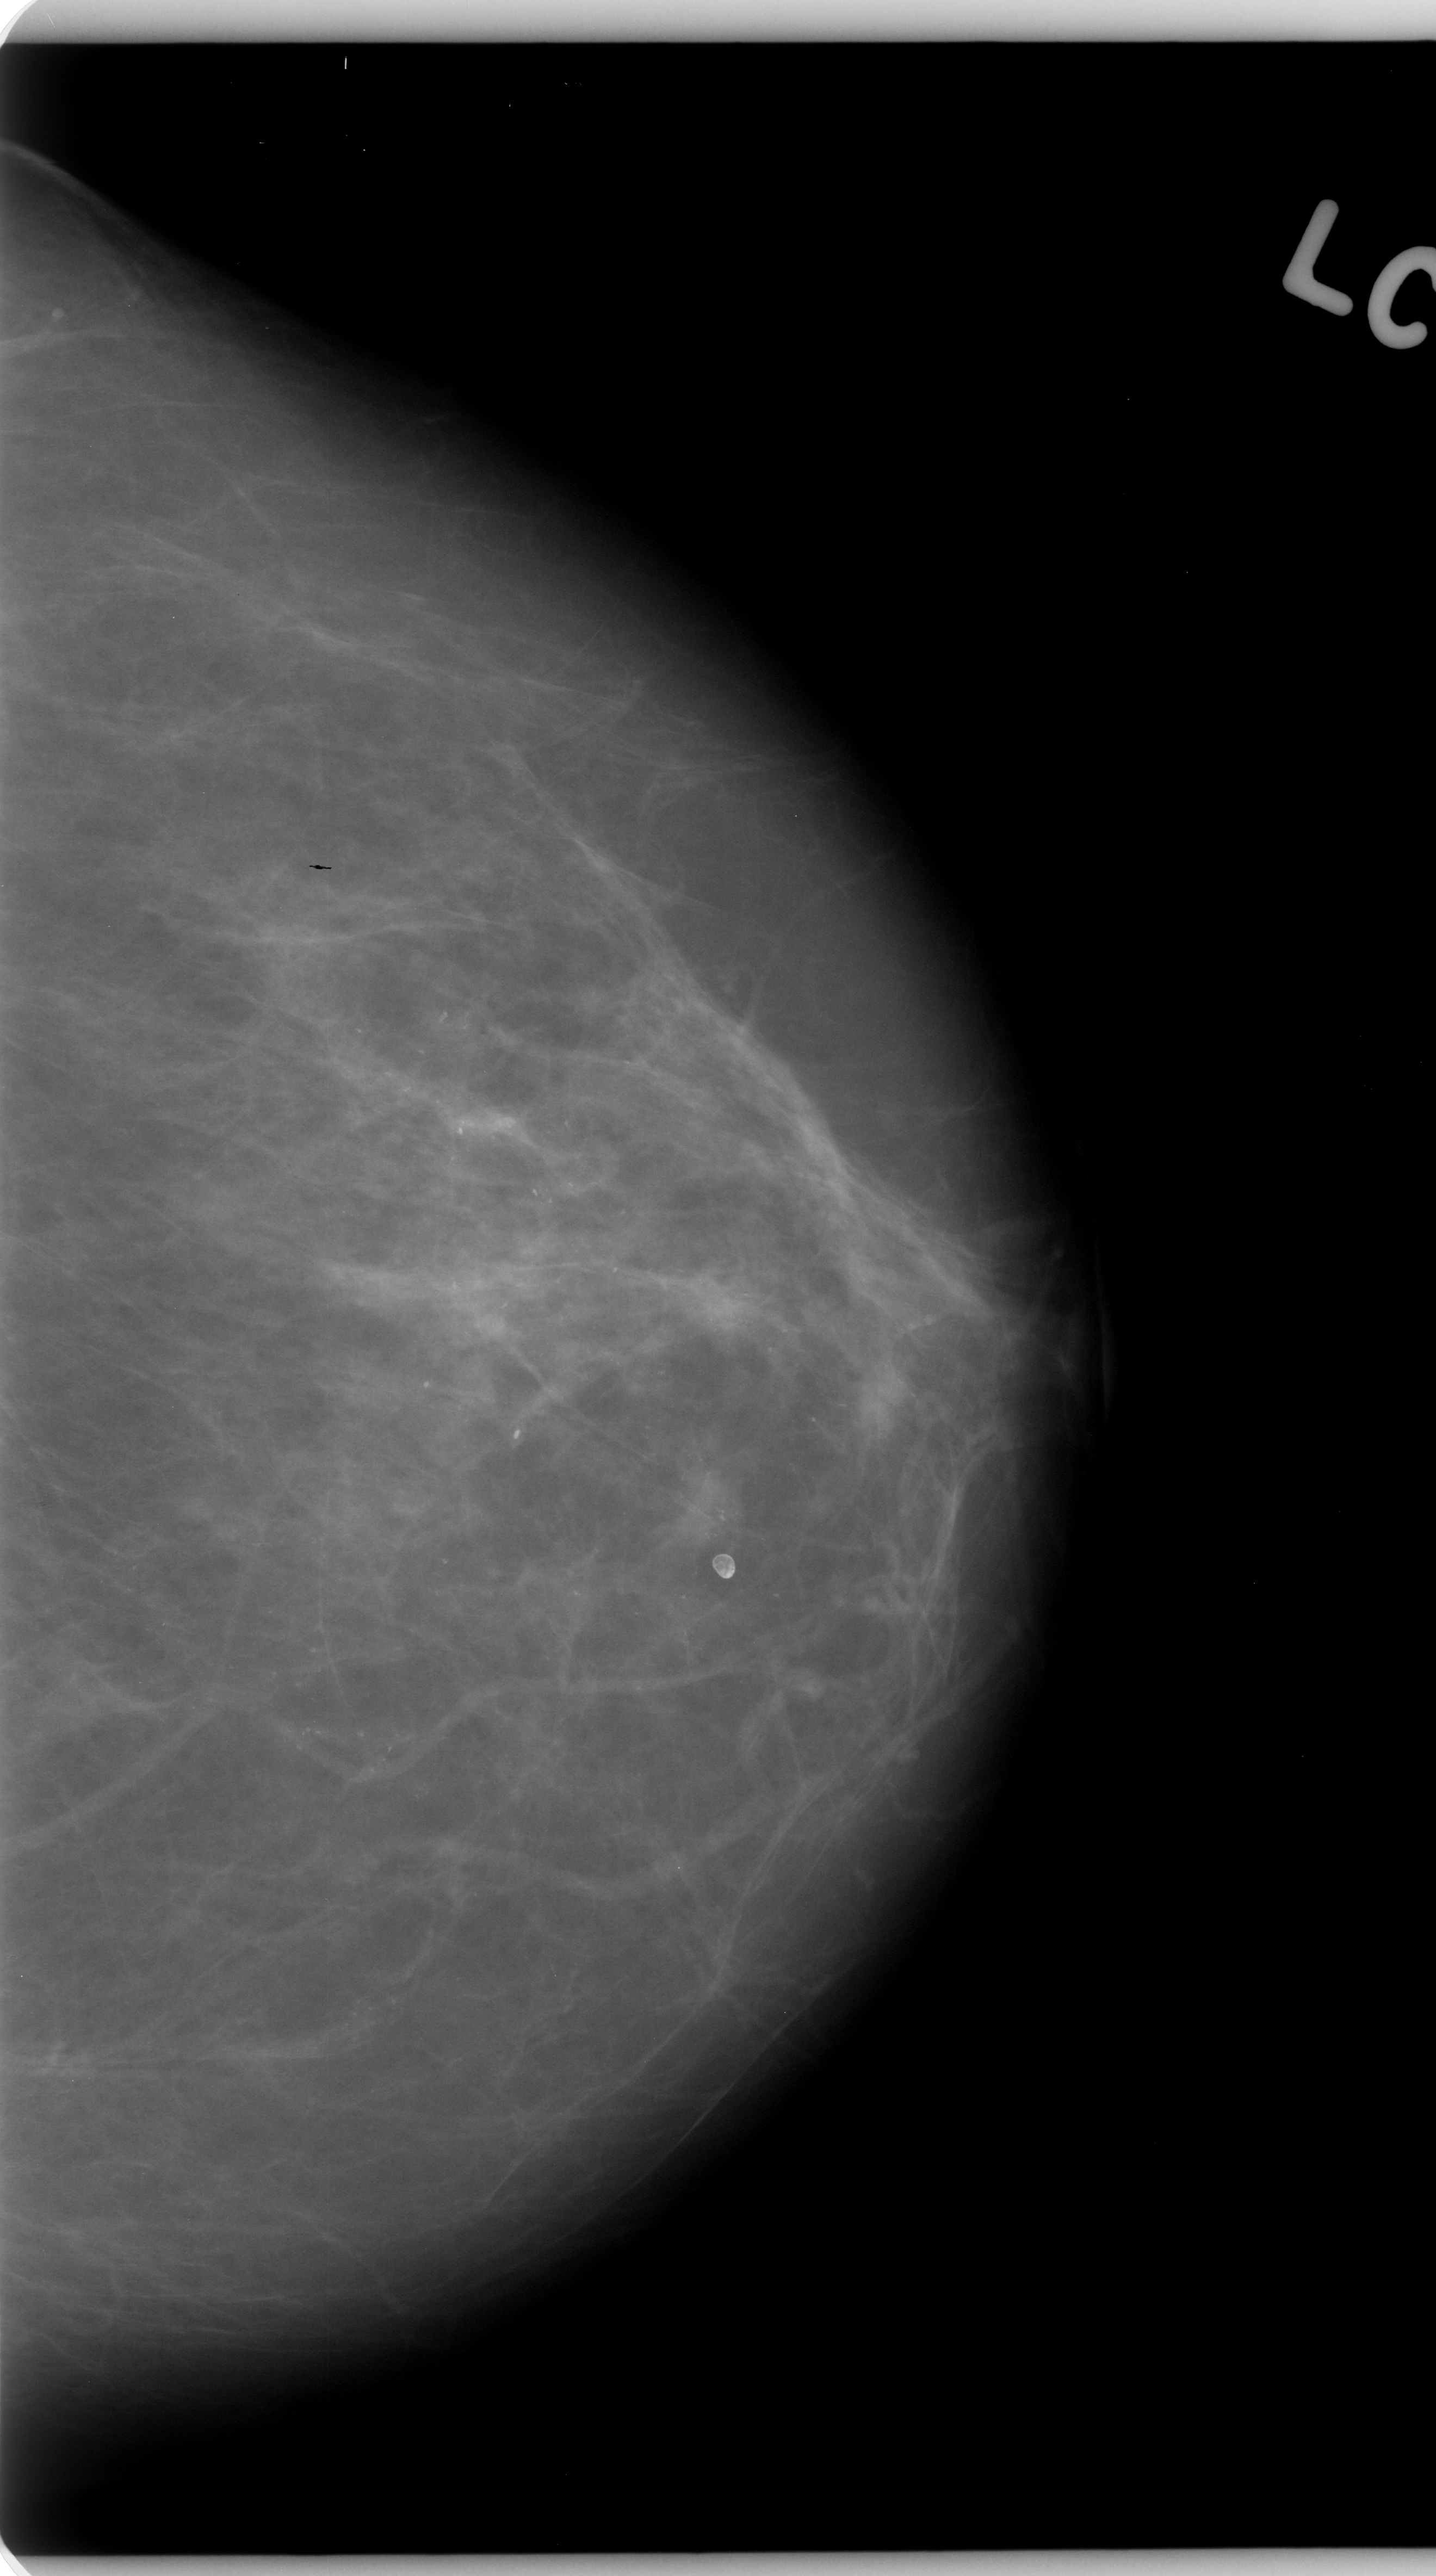
Mammogram (digitized film). Left breast. Craniocaudal (CC) view. Breast composition: almost entirely fatty (BI-RADS density category 1 of 4). 1436 × 2576 image matrix.
Expert-marked regions of interest on this film, with their recorded descriptors:
- calcifications, morphology amorphous, distribution regional; BI-RADS assessment category 5; pathology result (as recorded, not read from the image): malignant: bounding box <60,870,932,1755> (left, top, right, bottom; pixels)